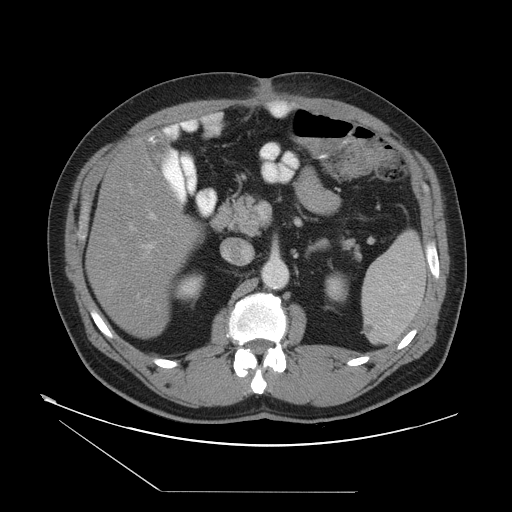
Contrast-enhanced abdominal CT, one axial slice. Slice 23 of 55 in the series (ordered by position). Intravenous contrast given. Soft-tissue window (W 400 / L 40 HU). 5 mm slice thickness. 512 × 512 image matrix, field of view 454 × 454 mm. Male patient, age 59 years. Case-level facts recorded for this patient, not image findings: diagnosis: colorectal cancer liver metastases, imaged before liver resection; multiple liver metastases: yes.
Annotated regions visible in this slice (expert manual segmentation):
- hepatic veins: bounding box (x1, y1, x2, y2) in pixels: (112, 142, 150, 301)
- liver: (88, 139, 201, 334)
- planned liver remnant (the part of the liver to remain after resection): (88, 139, 201, 334)
- portal vein (with intrahepatic branches): (141, 210, 170, 253)